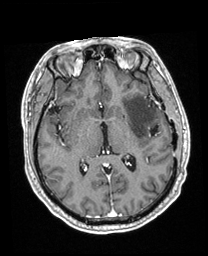
Brain MRI from a brain-tumour surgery series, one axial slice; position 108 of 208 along the scan axis; T1-weighted post-contrast; 208 × 256 image matrix, field of view 211 × 260 mm. From the clinical record (not read from this slice): histopathology: Astrocytoma; WHO grade: 3; IDH mutation: yes.
Annotated regions visible in this slice (expert manual segmentation):
- previous resection cavity: box from (x=151, y=125) to (x=159, y=137) px